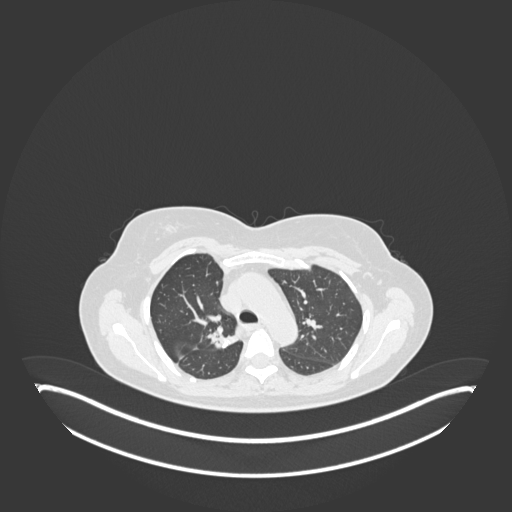
Chest CT, one axial slice. Slice 123 of 181 in the series (ordered by position). Reconstruction kernel B30f. Lung window (W 1500 / L -600 HU). 1 mm slice thickness. 512 × 512 image matrix. Patient: female, 65 years. Case-level facts recorded for this patient, not image findings: clinical TNM (as recorded): T1b N0 M0; histopathological grade: G2.
Outlined on this slice (bounding box drawn by a radiologist):
- lung tumour (recorded histology: adenocarcinoma): bounding box <206,327,240,350> (left, top, right, bottom; pixels)